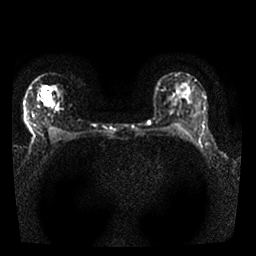
Breast MRI, one axial slice; position 18 of 25 along the scan axis; diffusion-weighted series; image 2 of 4 stored at this slice position (different b-values; order by instance number); 1.5 T; 4 mm slice thickness; 256 × 256 image matrix, field of view 310 × 310 mm. Female patient.
Structures marked on this image (expert manual segmentation):
- tumour on diffusion-weighted imaging: box from (x=39, y=93) to (x=49, y=99) px